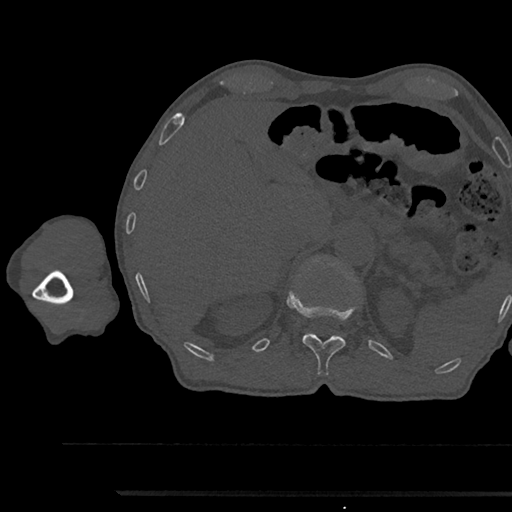
CT including the spine, one axial slice. Slice 696 of 797 in the series (ordered by position). 120 kVp. Bone window (W 1800 / L 400 HU). 0.5 mm slice thickness. 512 × 512 image matrix, field of view 367 × 367 mm. Male patient, age 79 years. From the clinical record (not read from this slice): primary cancer: prostate.
Structures marked on this image (semi-automatically segmented with operator editing):
- T12 vertebra: box from (x=288, y=294) to (x=350, y=375) px